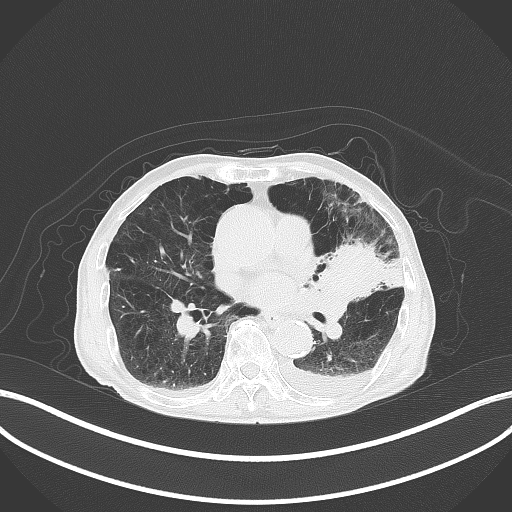
Chest CT, one axial slice. Slice 185 of 227 in the series (ordered by position). 120 kVp. Lung window (W 1500 / L -600 HU). 512 × 512 image matrix, field of view 400 × 400 mm. Patient: male, 90 years or older. From the clinical record (not read from this slice): clinical TNM (as recorded): T2b N1 M0.
Outlined on this slice (rectangle marked by the reading radiologist):
- lung tumour (recorded histology: squamous cell carcinoma): bounding box [x1, y1, x2, y2] px = [307, 244, 402, 301]